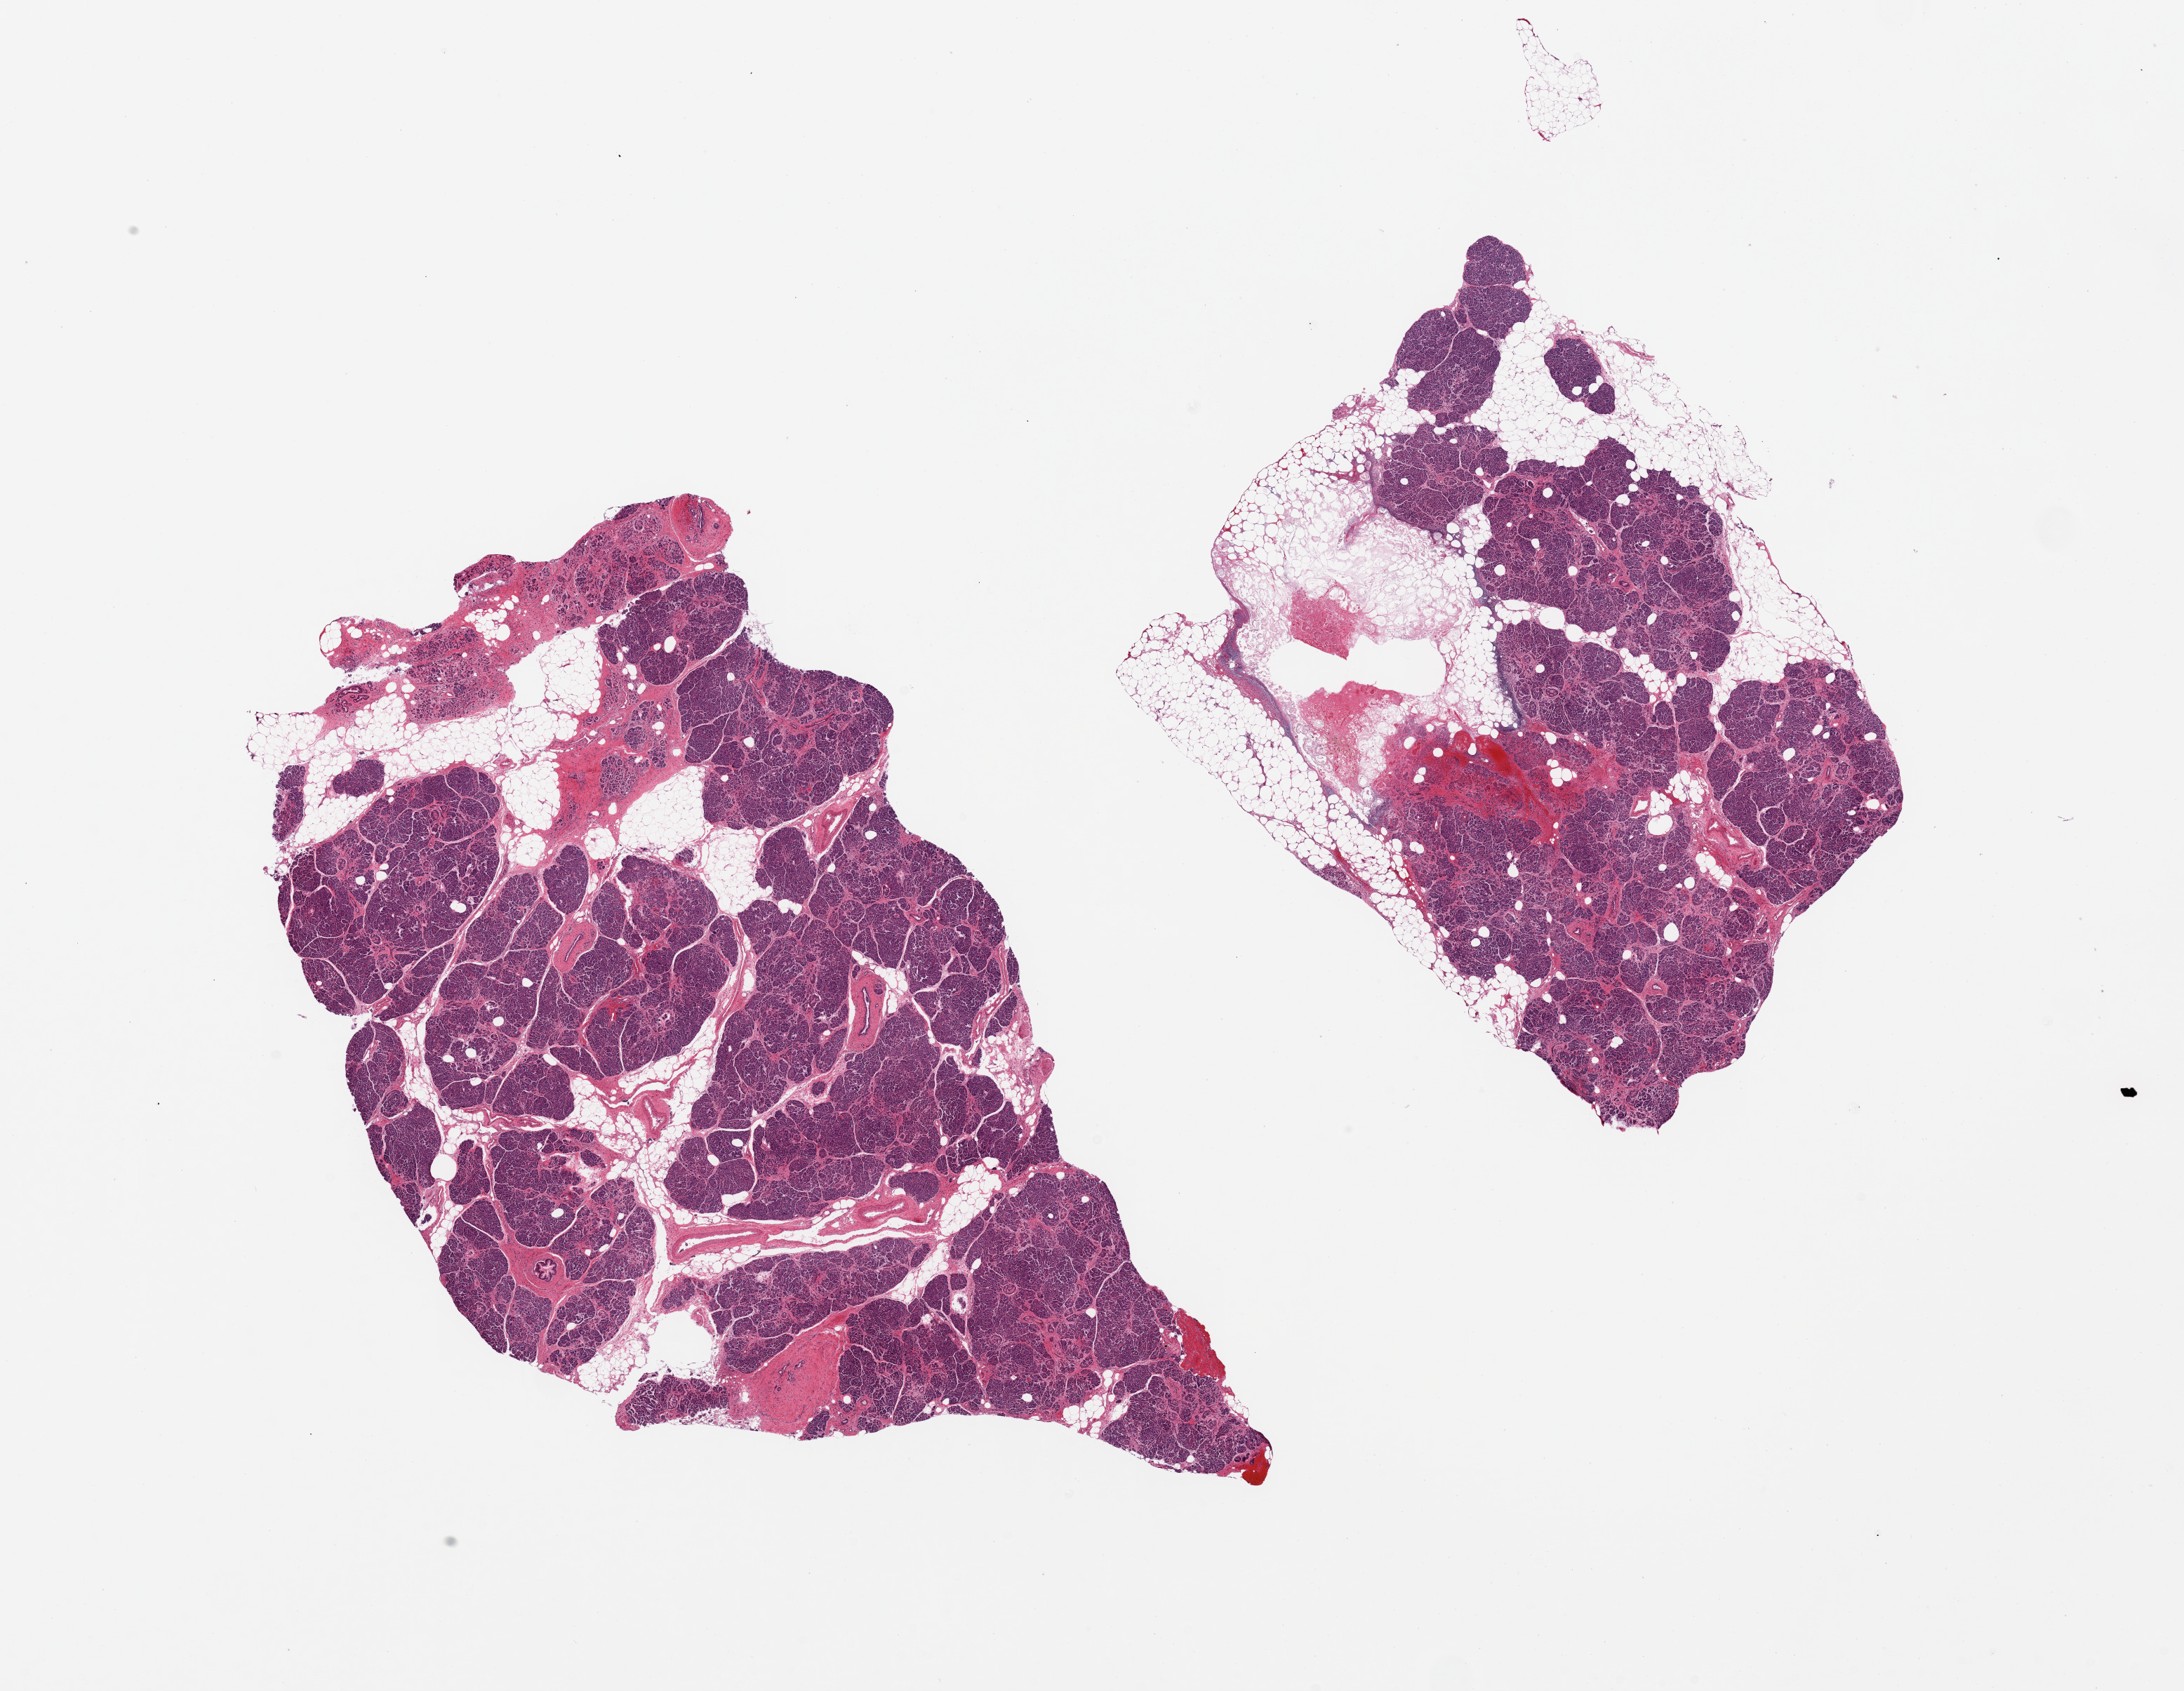
Digitized haematoxylin and eosin-stained section — whole scanned area (about 24.6 x 19.1 mm, from a 20x scan) shown as a low-resolution overview. PAXgene-fixed, paraffin-embedded tissue. Sampled site (target tissue): pancreas. Tissue donor sample. Female donor.
Pathologist's review note for this sample: 2 pieces, specimen is ~ 30-40% internal and attached adipose tissue, some fibrosis and atrophy, focal PanIN.